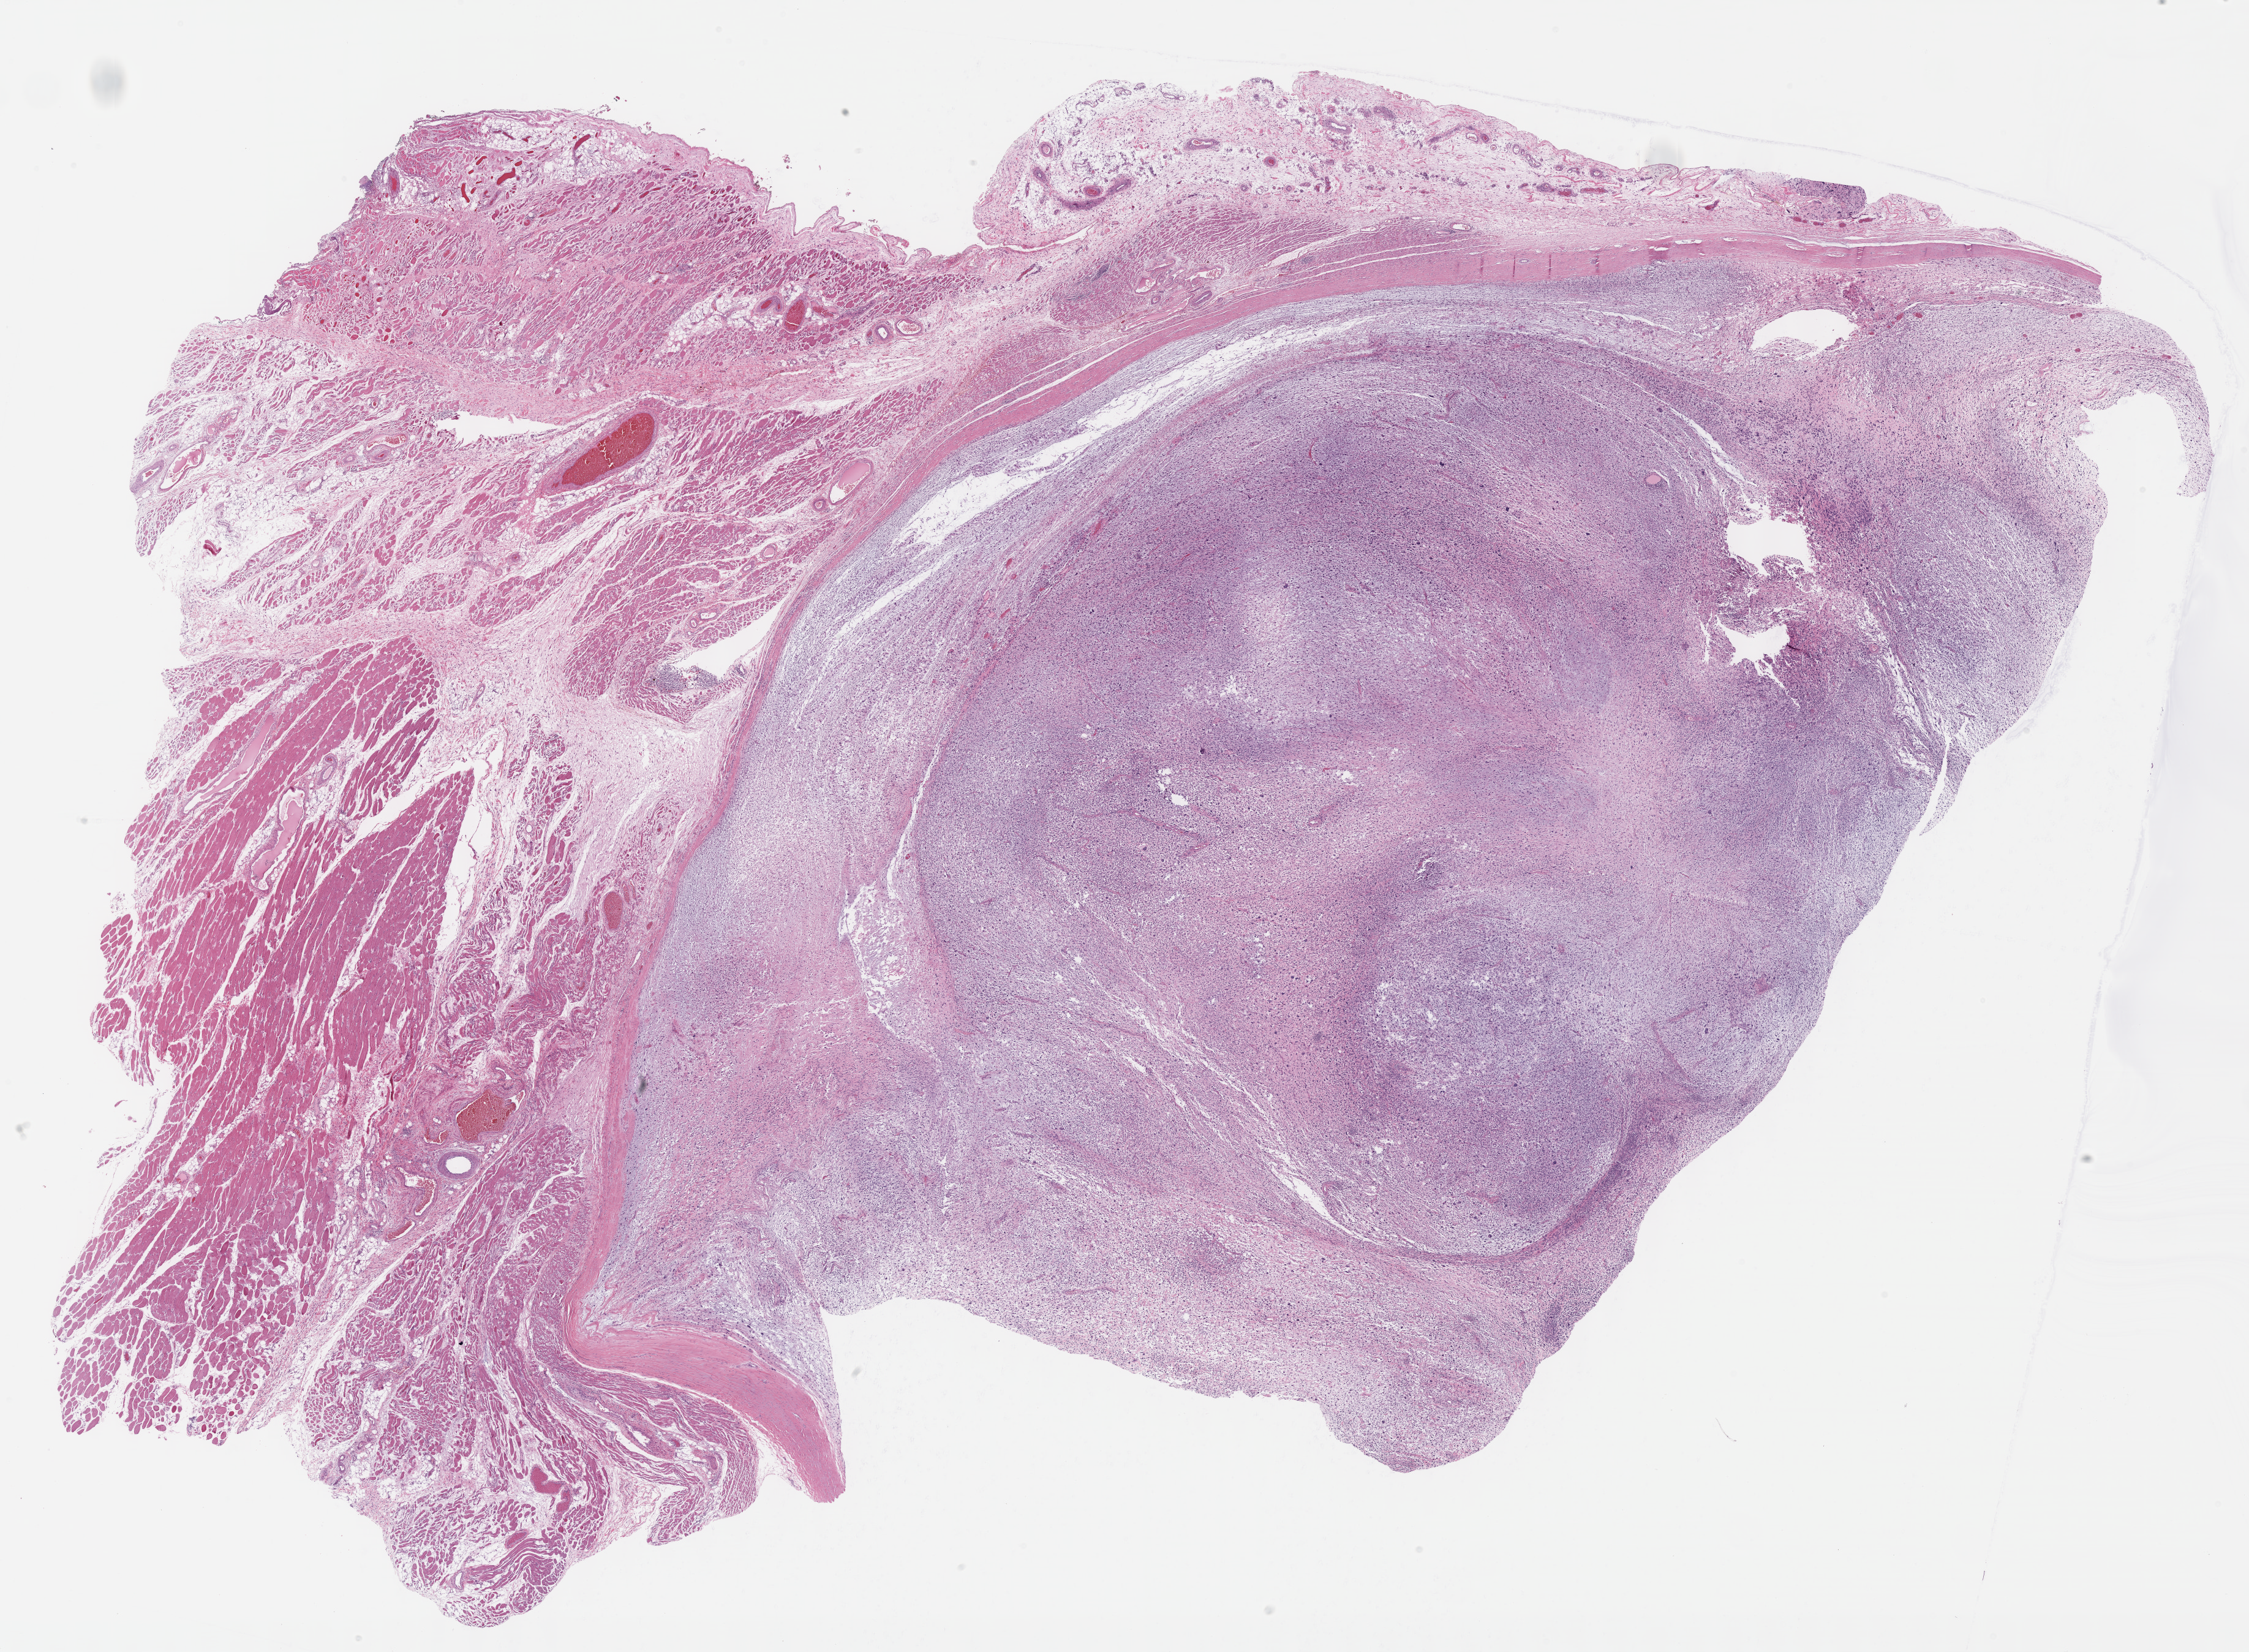
Digitized H&E-stained tissue section (whole slide), low-resolution overview of the scanned area, about 29.7 x 21.8 mm (from a 40x scan). FFPE section. Primary tumour sample from the connective, subcutaneous and other soft tissues. Female patient; age at initial diagnosis 83 years.
* diagnosis: Fibromyxosarcoma (connective, subcutaneous and other soft tissues of lower limb and hip)